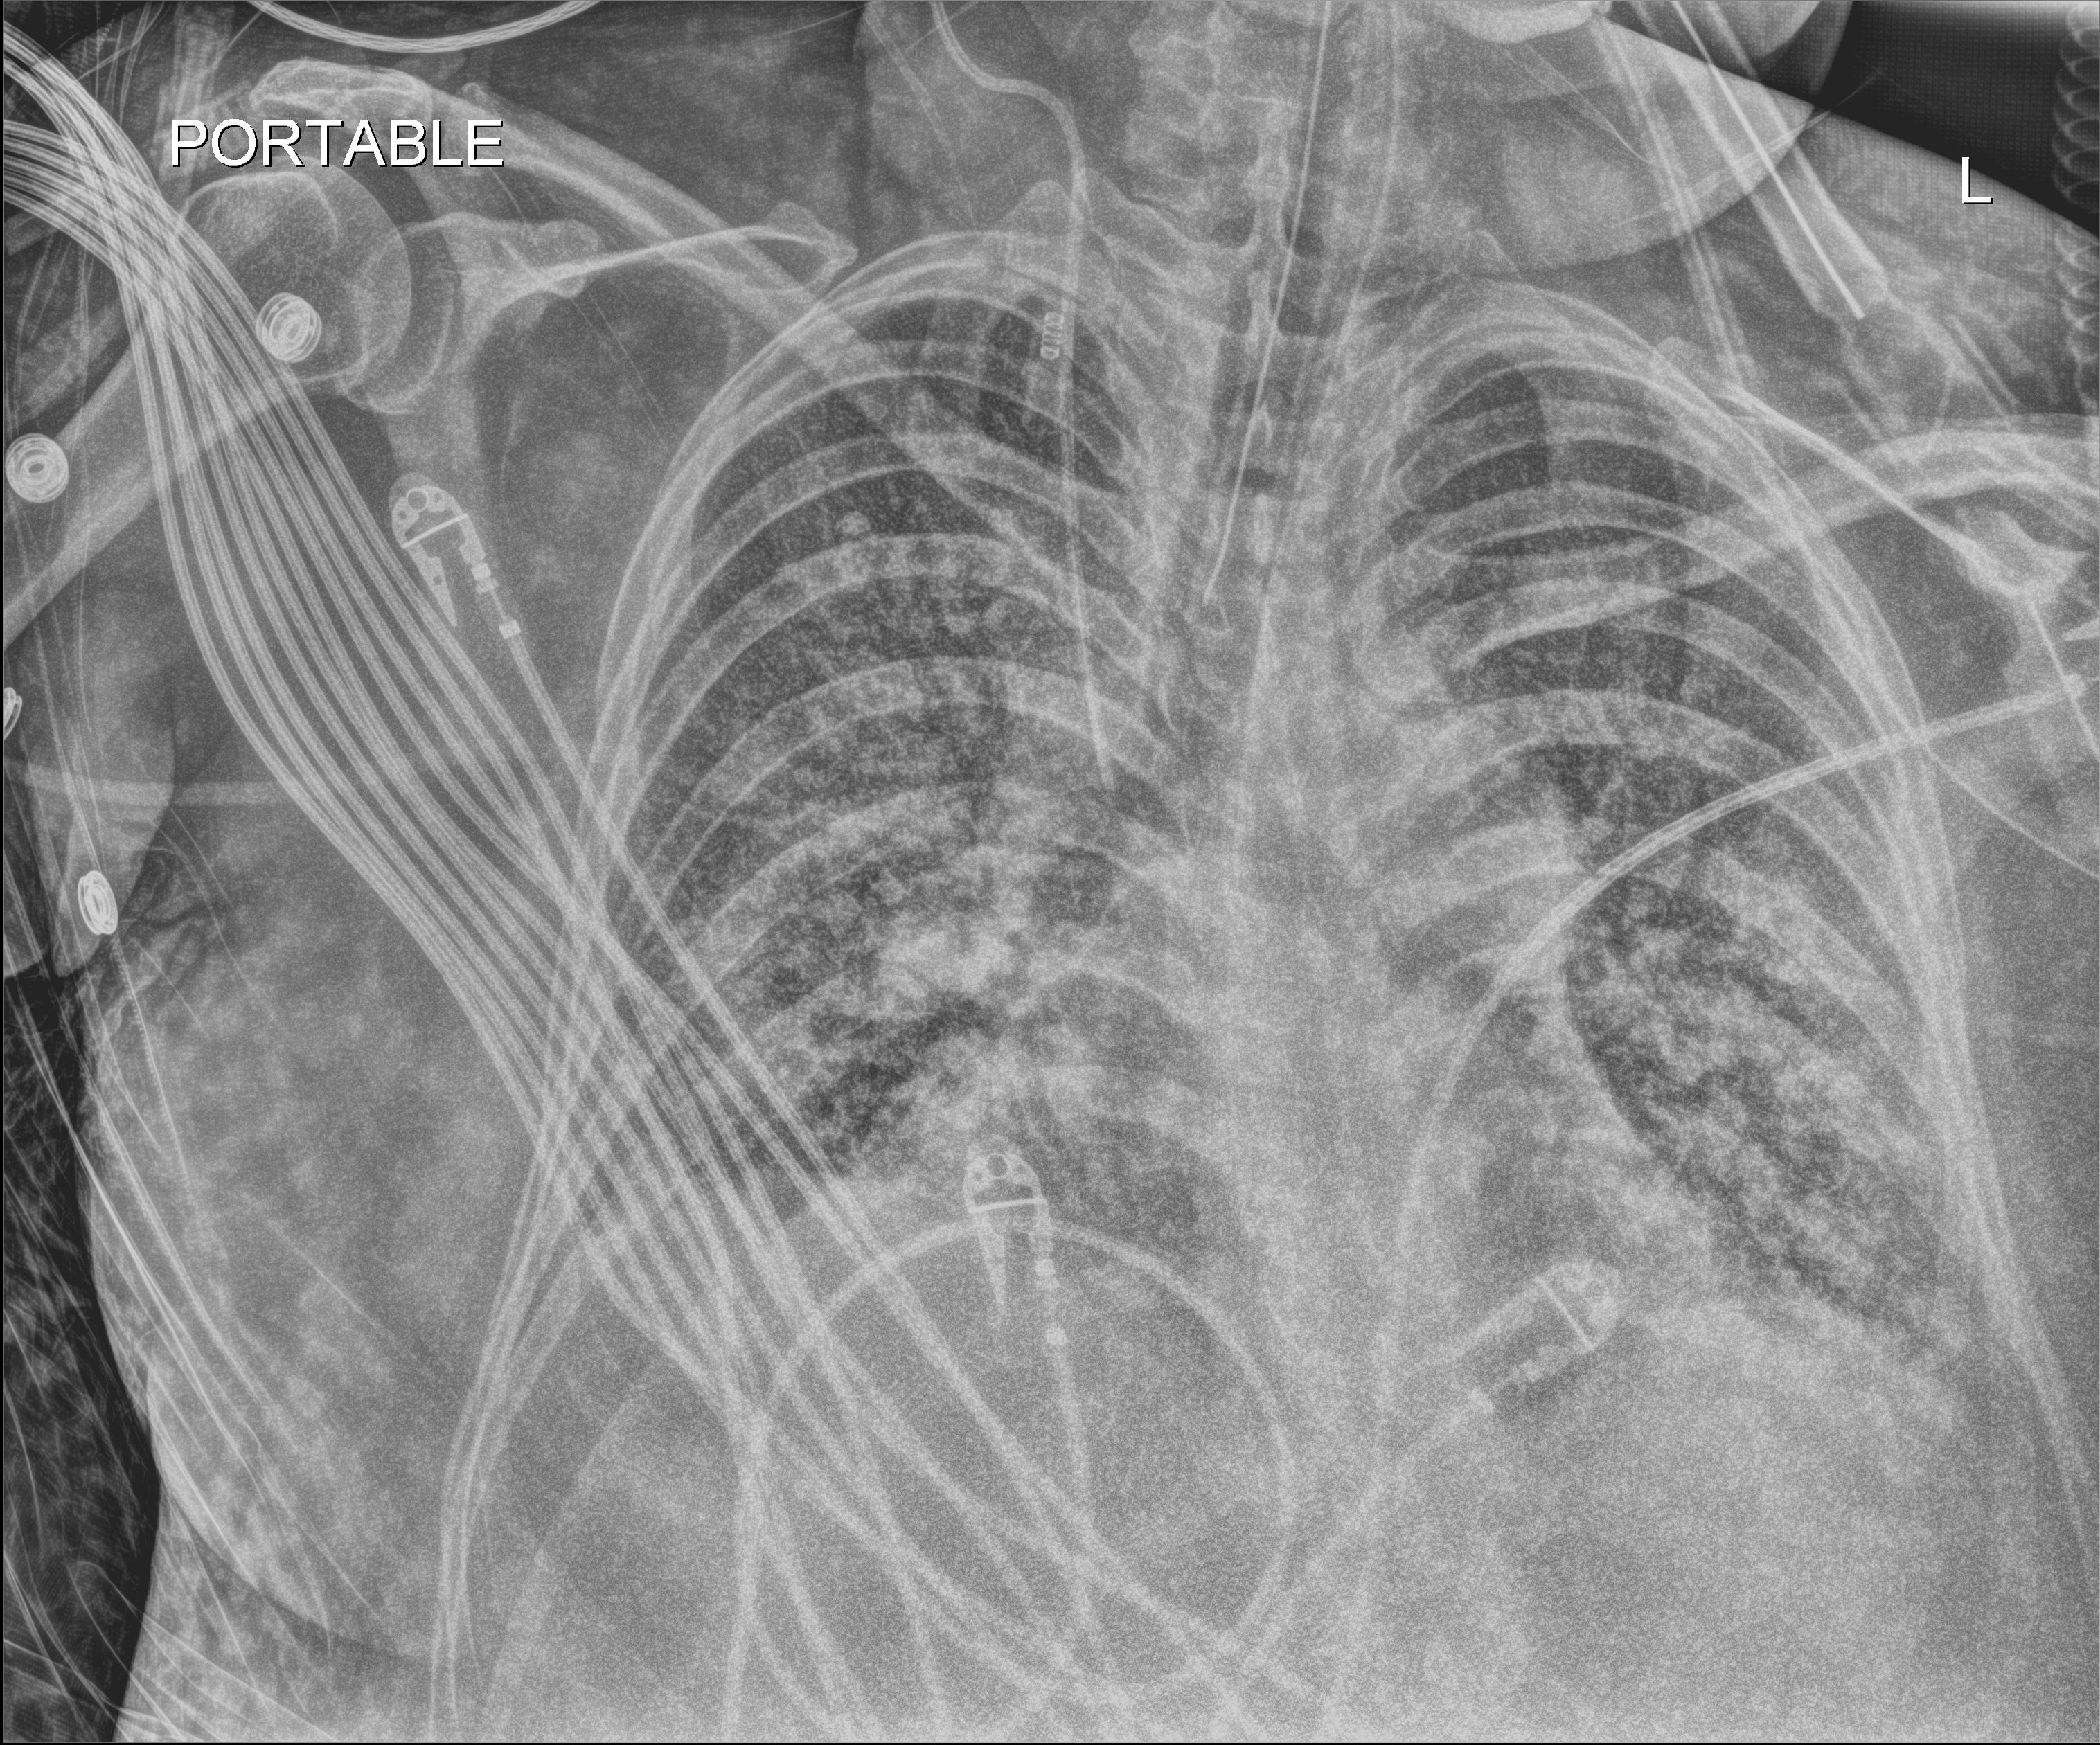
Bedside chest radiograph (digital radiography), anteroposterior (AP) projection. Adult patient hospitalised with COVID-19, age 18–59 years.
From the hospital-stay record, not from the radiograph (when in the stay this image was taken is not recorded): mechanically ventilated during this hospital stay: yes; smoking status (admission record): never.